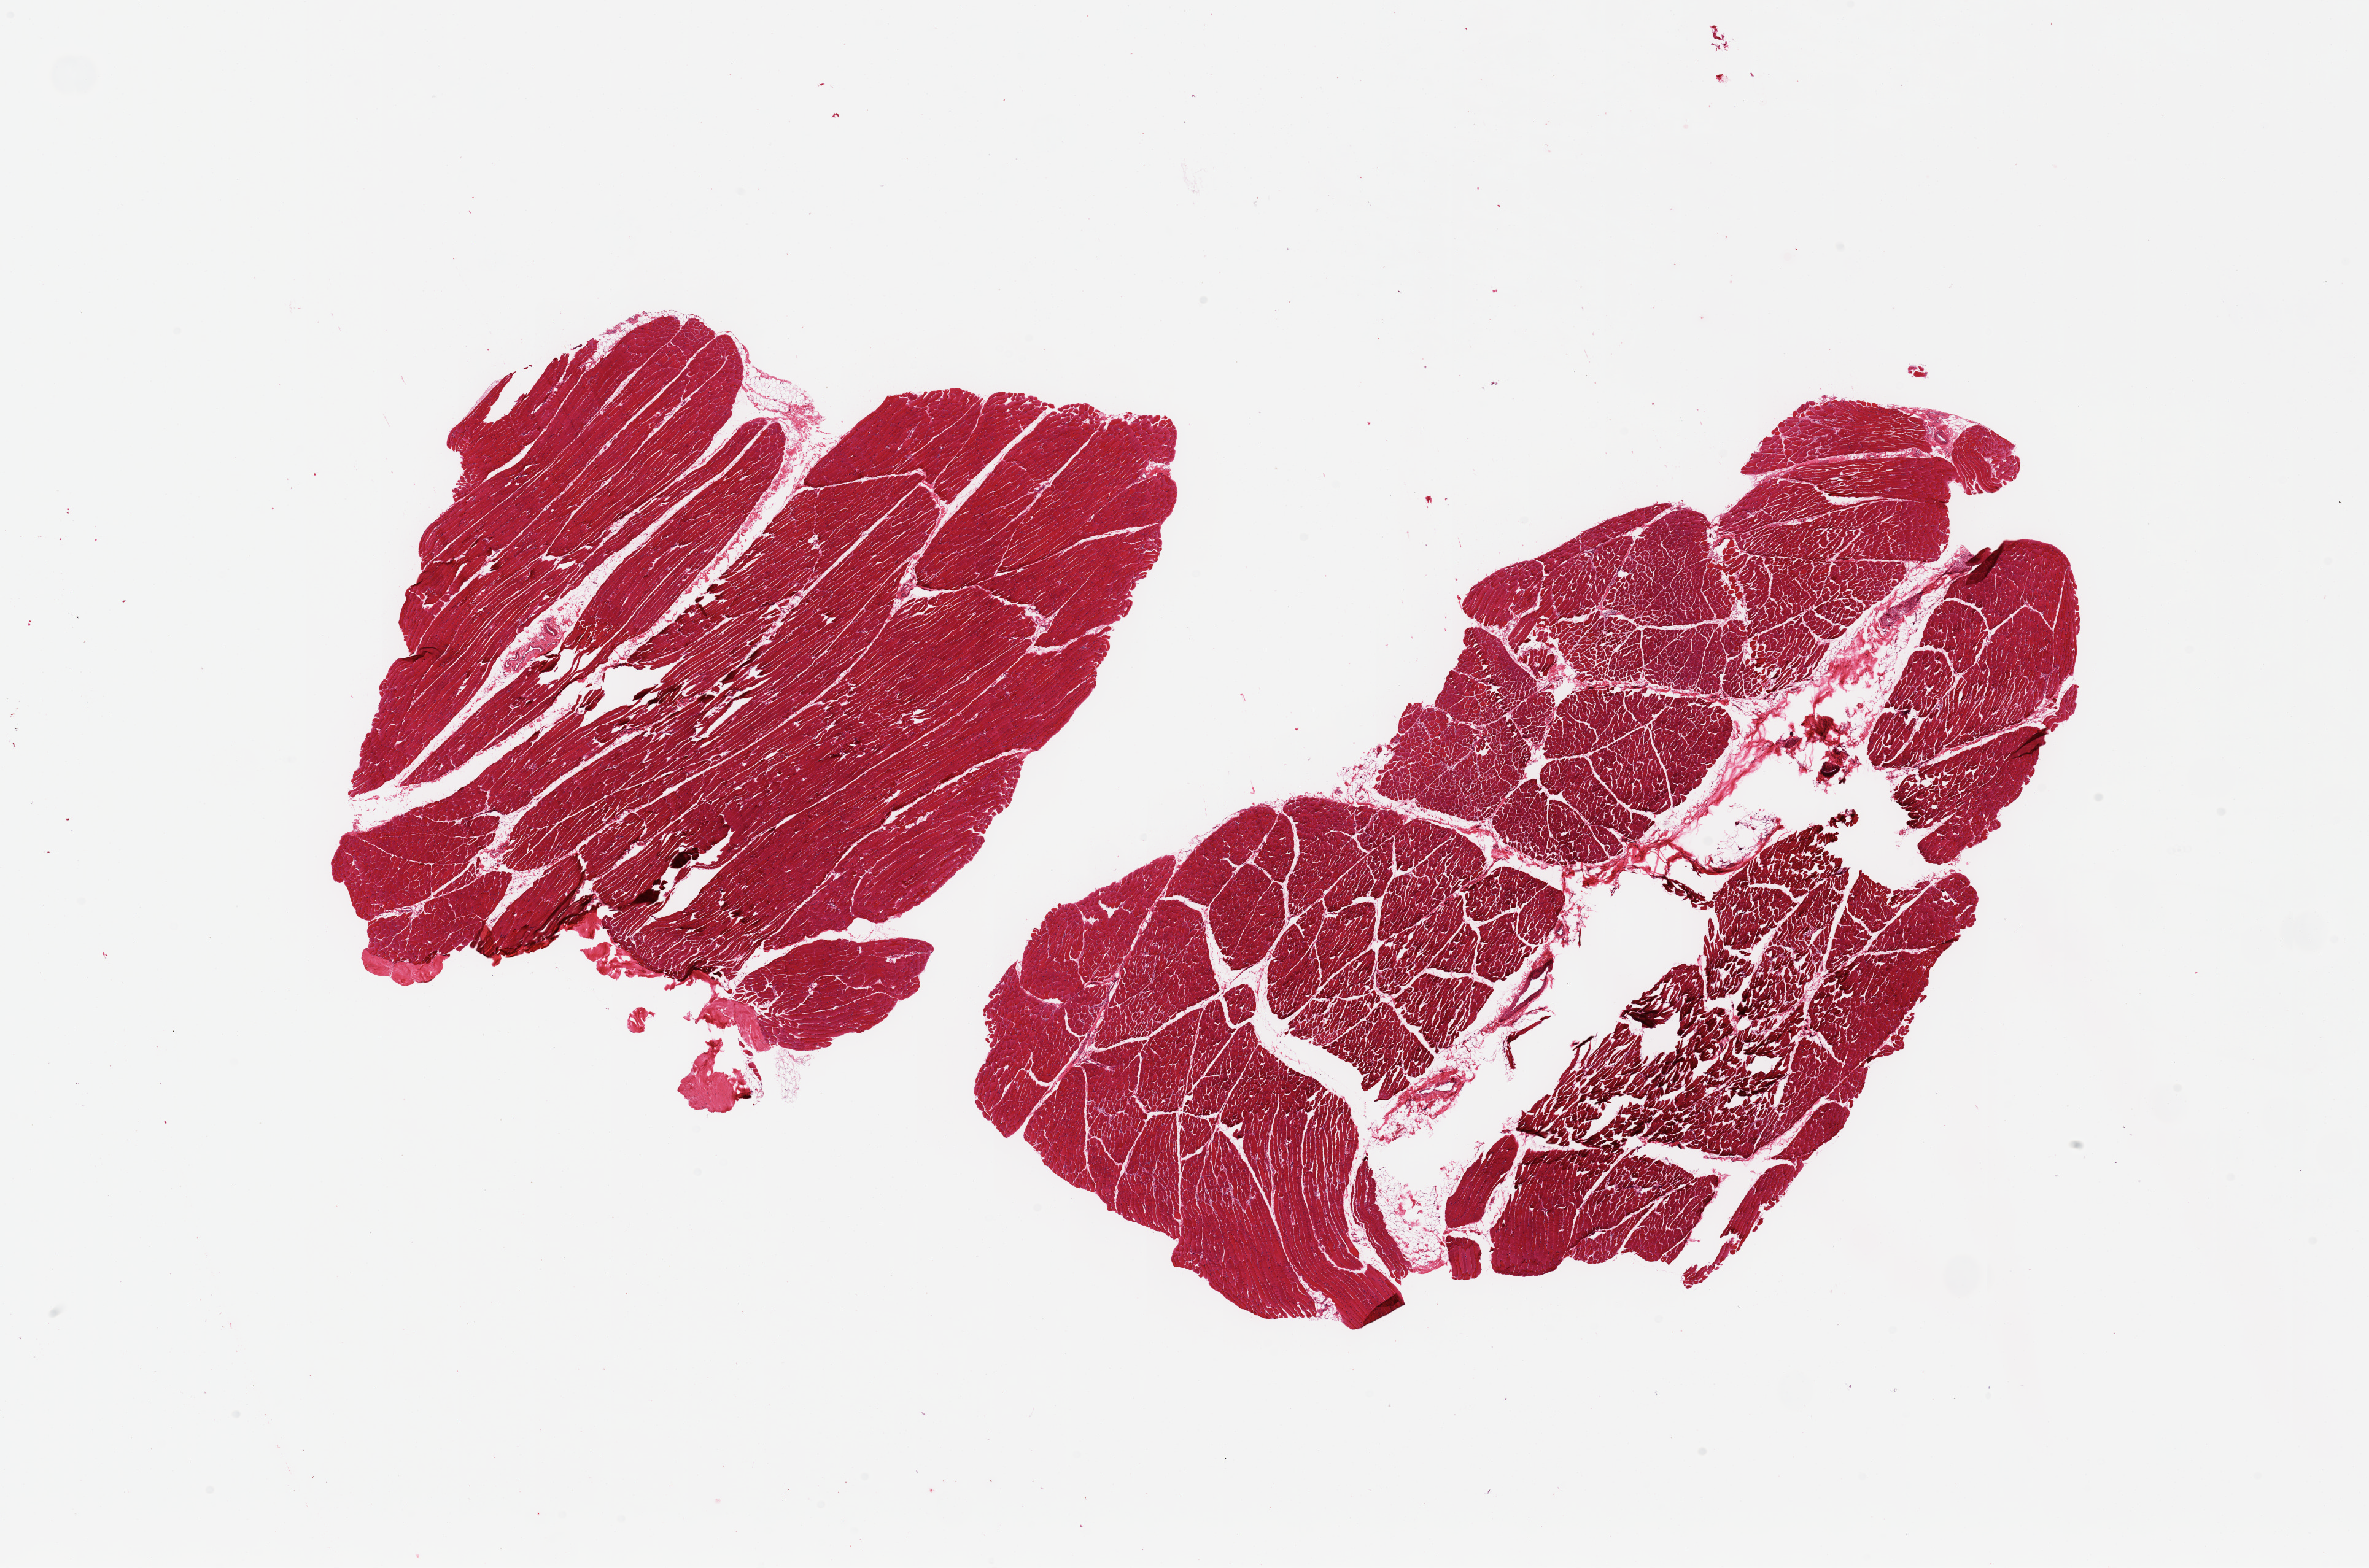
Digitized H&E-stained section, brightfield, shown as a low-resolution overview of the whole scanned area (about 30.5 x 20.2 mm), PAXgene-fixed paraffin-embedded (PFPE) section, section of skeletal muscle (target tissue), donor tissue sample.
Pathologist's review note for this sample: 2 pieces, ~5-10% interstitial fat.